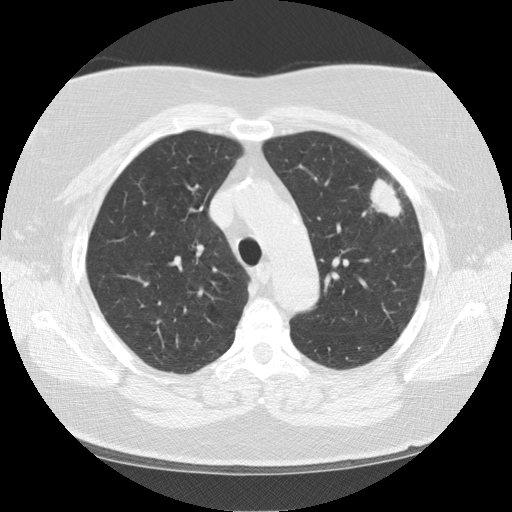
Low-dose screening chest CT, one axial slice; position 96 of 130 along the scan axis; 120 kVp; lung window (W 1500 / L -600 HU); 2.5 mm slice thickness; 512 × 512 image matrix, field of view 350 × 350 mm.
Annotated regions visible in this slice (manually delineated by an expert):
- lesion 1 (tumor, upper lobe of left lung): bounding box <370,179,402,217> (left, top, right, bottom; pixels)